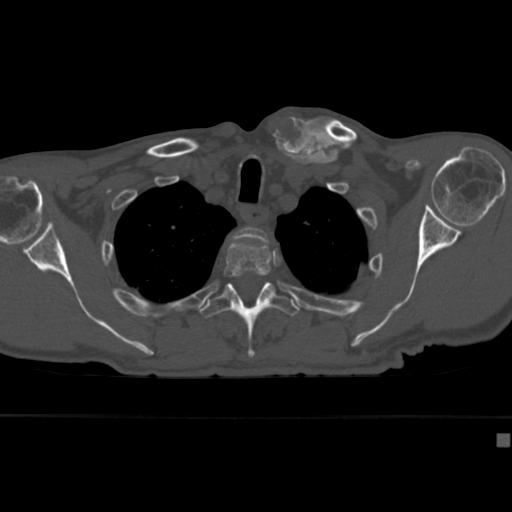
CT including the spine, one axial slice. Position 328 of 430 along the scan axis. Bone window (W 1800 / L 400 HU). 1.5 mm slice thickness. 512 × 512 image matrix, field of view 337 × 337 mm. Male patient, age 64 years. From the clinical record (not read from this slice): primary cancer: uterus; vertebrae with lytic lesions (as recorded): T1, T4, T5, T7, L5.
Outlined on this slice (semi-automatic segmentation, software-assisted and operator-edited):
- T2 vertebra: bounding box (x1, y1, x2, y2) in pixels: (233, 227, 269, 242)
- T3 vertebra: (223, 242, 271, 284)
- T4 vertebra: (201, 282, 300, 358)